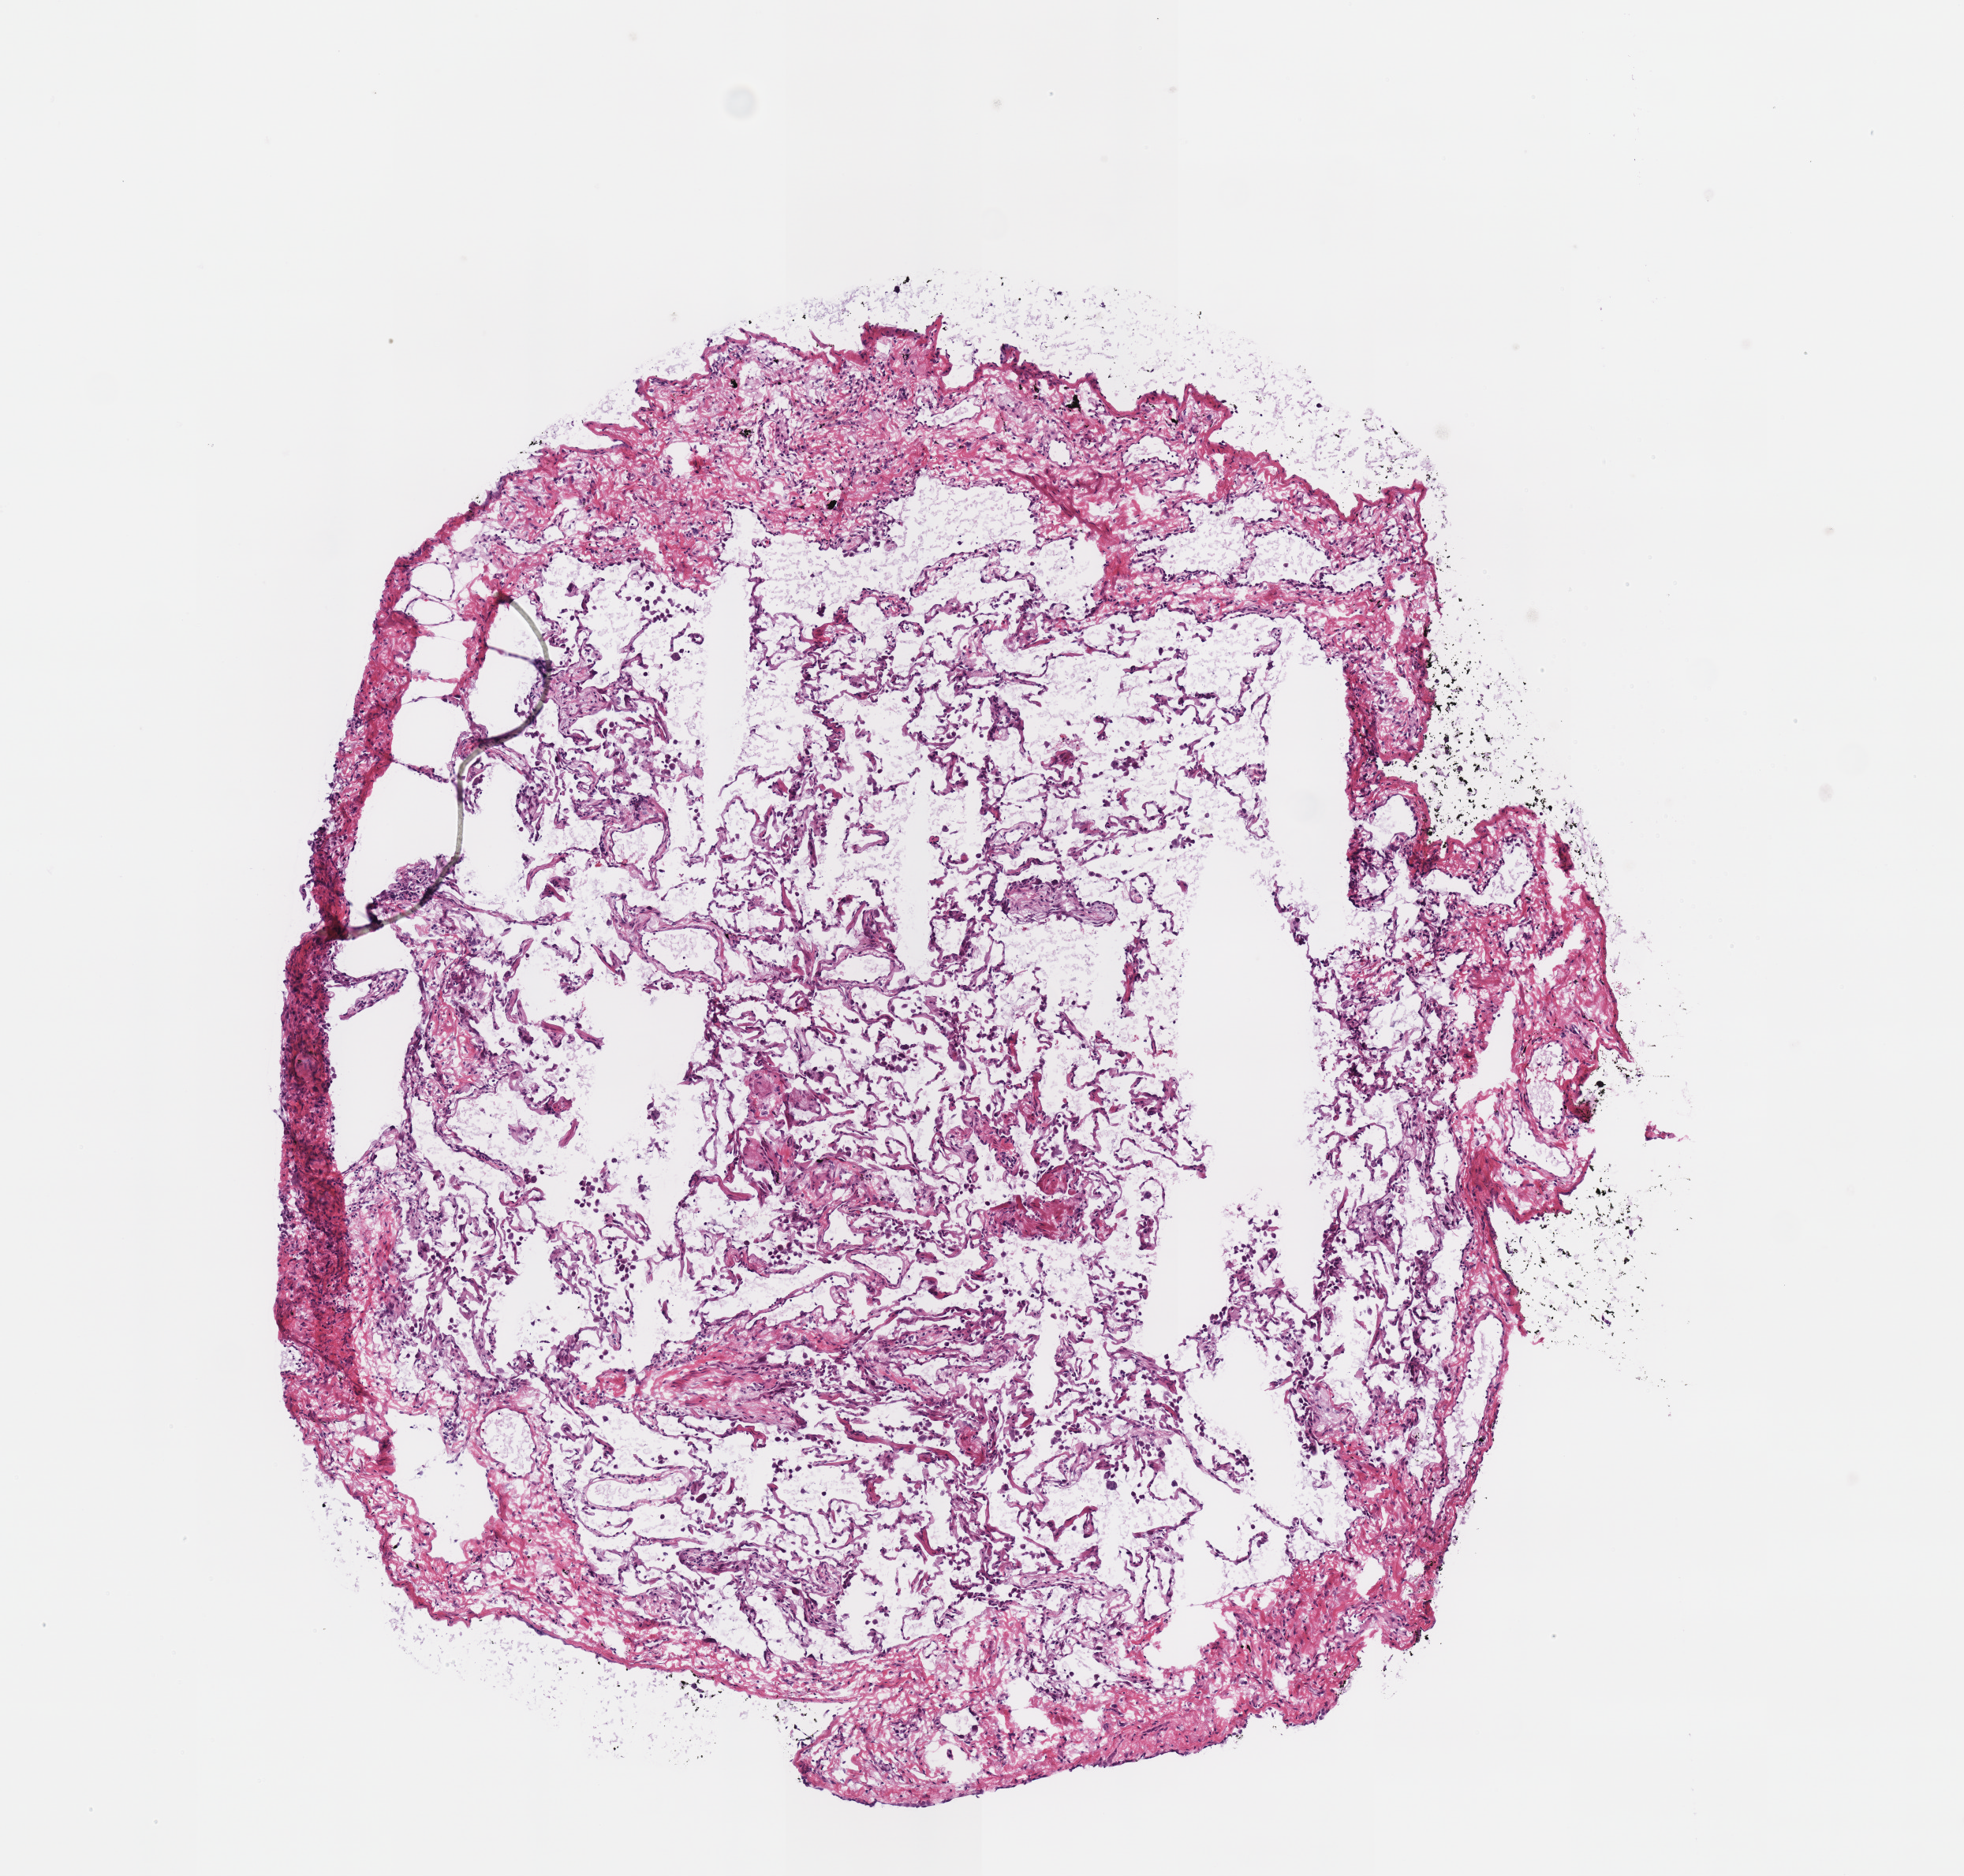
Whole-slide histology image, Hematoxylin and eosin (H&E) stained, a low-resolution overview of the entire scanned area, about 4.9 x 4.7 mm (acquisition: 40x scan). Frozen section from the top of the tissue portion. Lung, solid tissue normal (non-tumour tissue) sample. Patient: male, age at initial diagnosis 84 years.
This section: solid tissue normal sample (biorepository sample class). Patient diagnosis: Squamous cell carcinoma, NOS (lower lobe, lung).